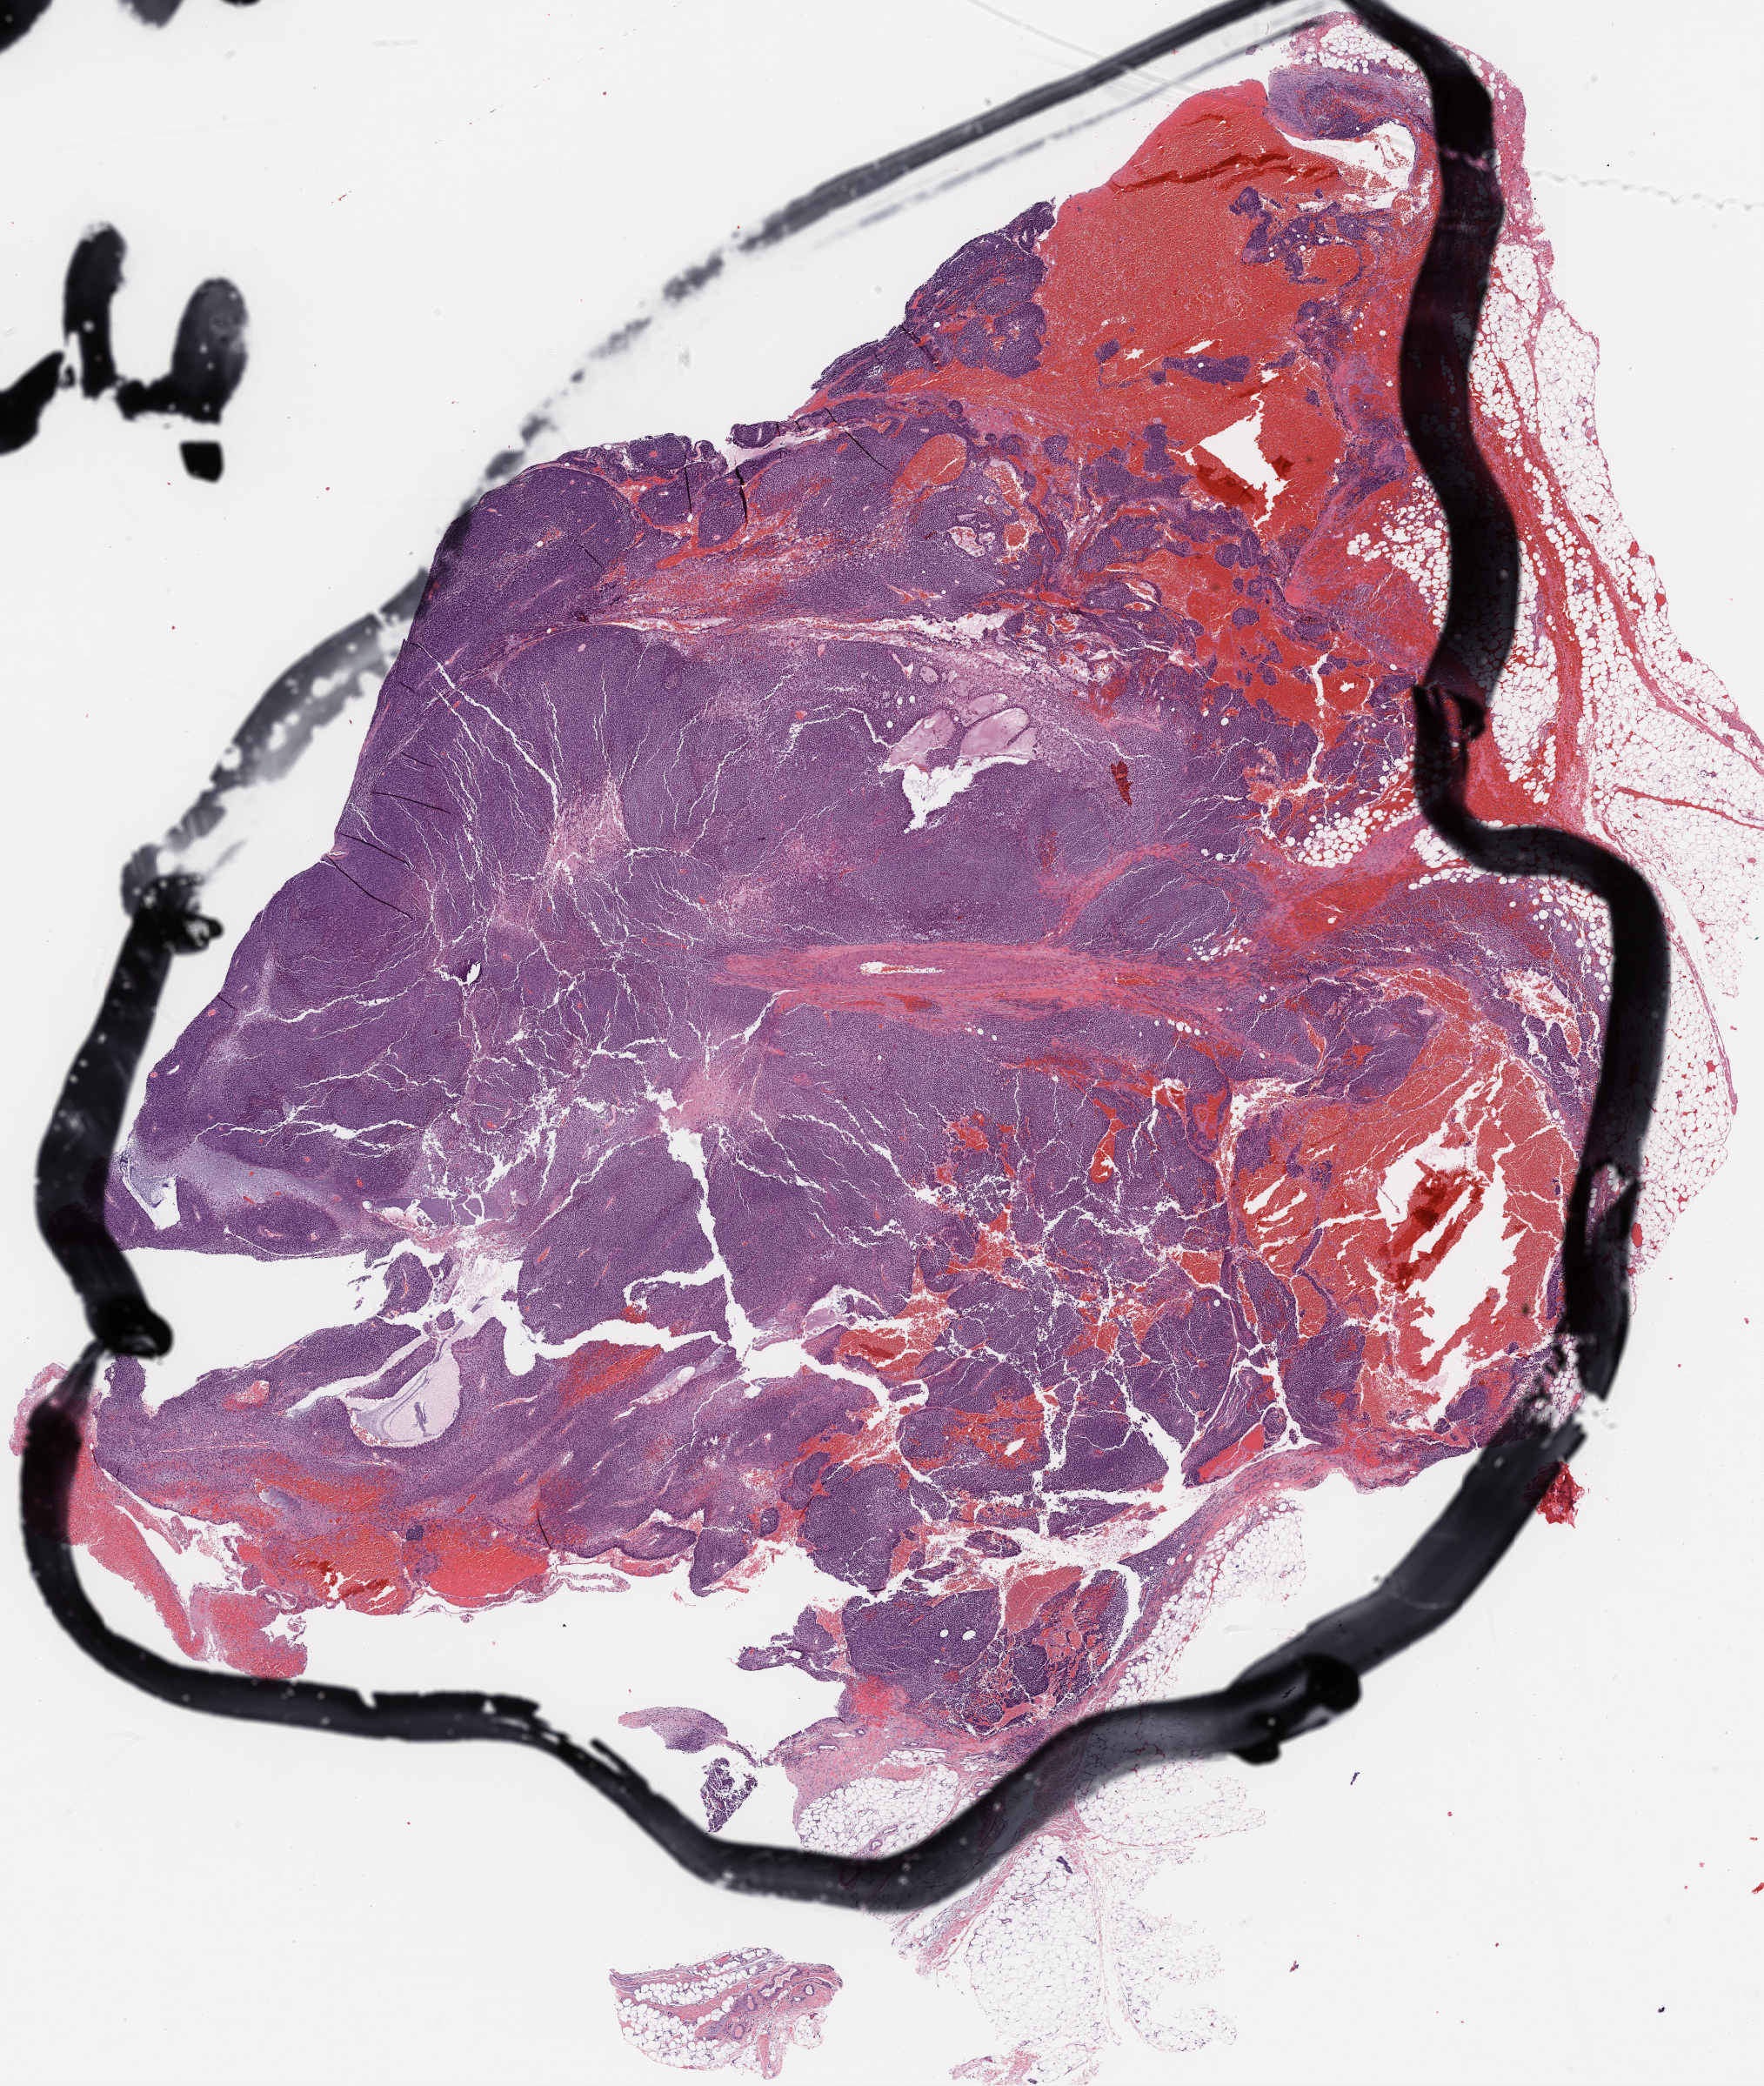
H&E whole-slide image, whole scanned area (about 16.4 x 19.3 mm, from a 20x scan) shown as a low-resolution overview, formalin-fixed paraffin-embedded (FFPE) diagnostic section, metastatic tumour sample. Male patient; age at initial diagnosis 60 years.
This section: metastatic tumour tissue. Patient diagnosis: Malignant melanoma, NOS.